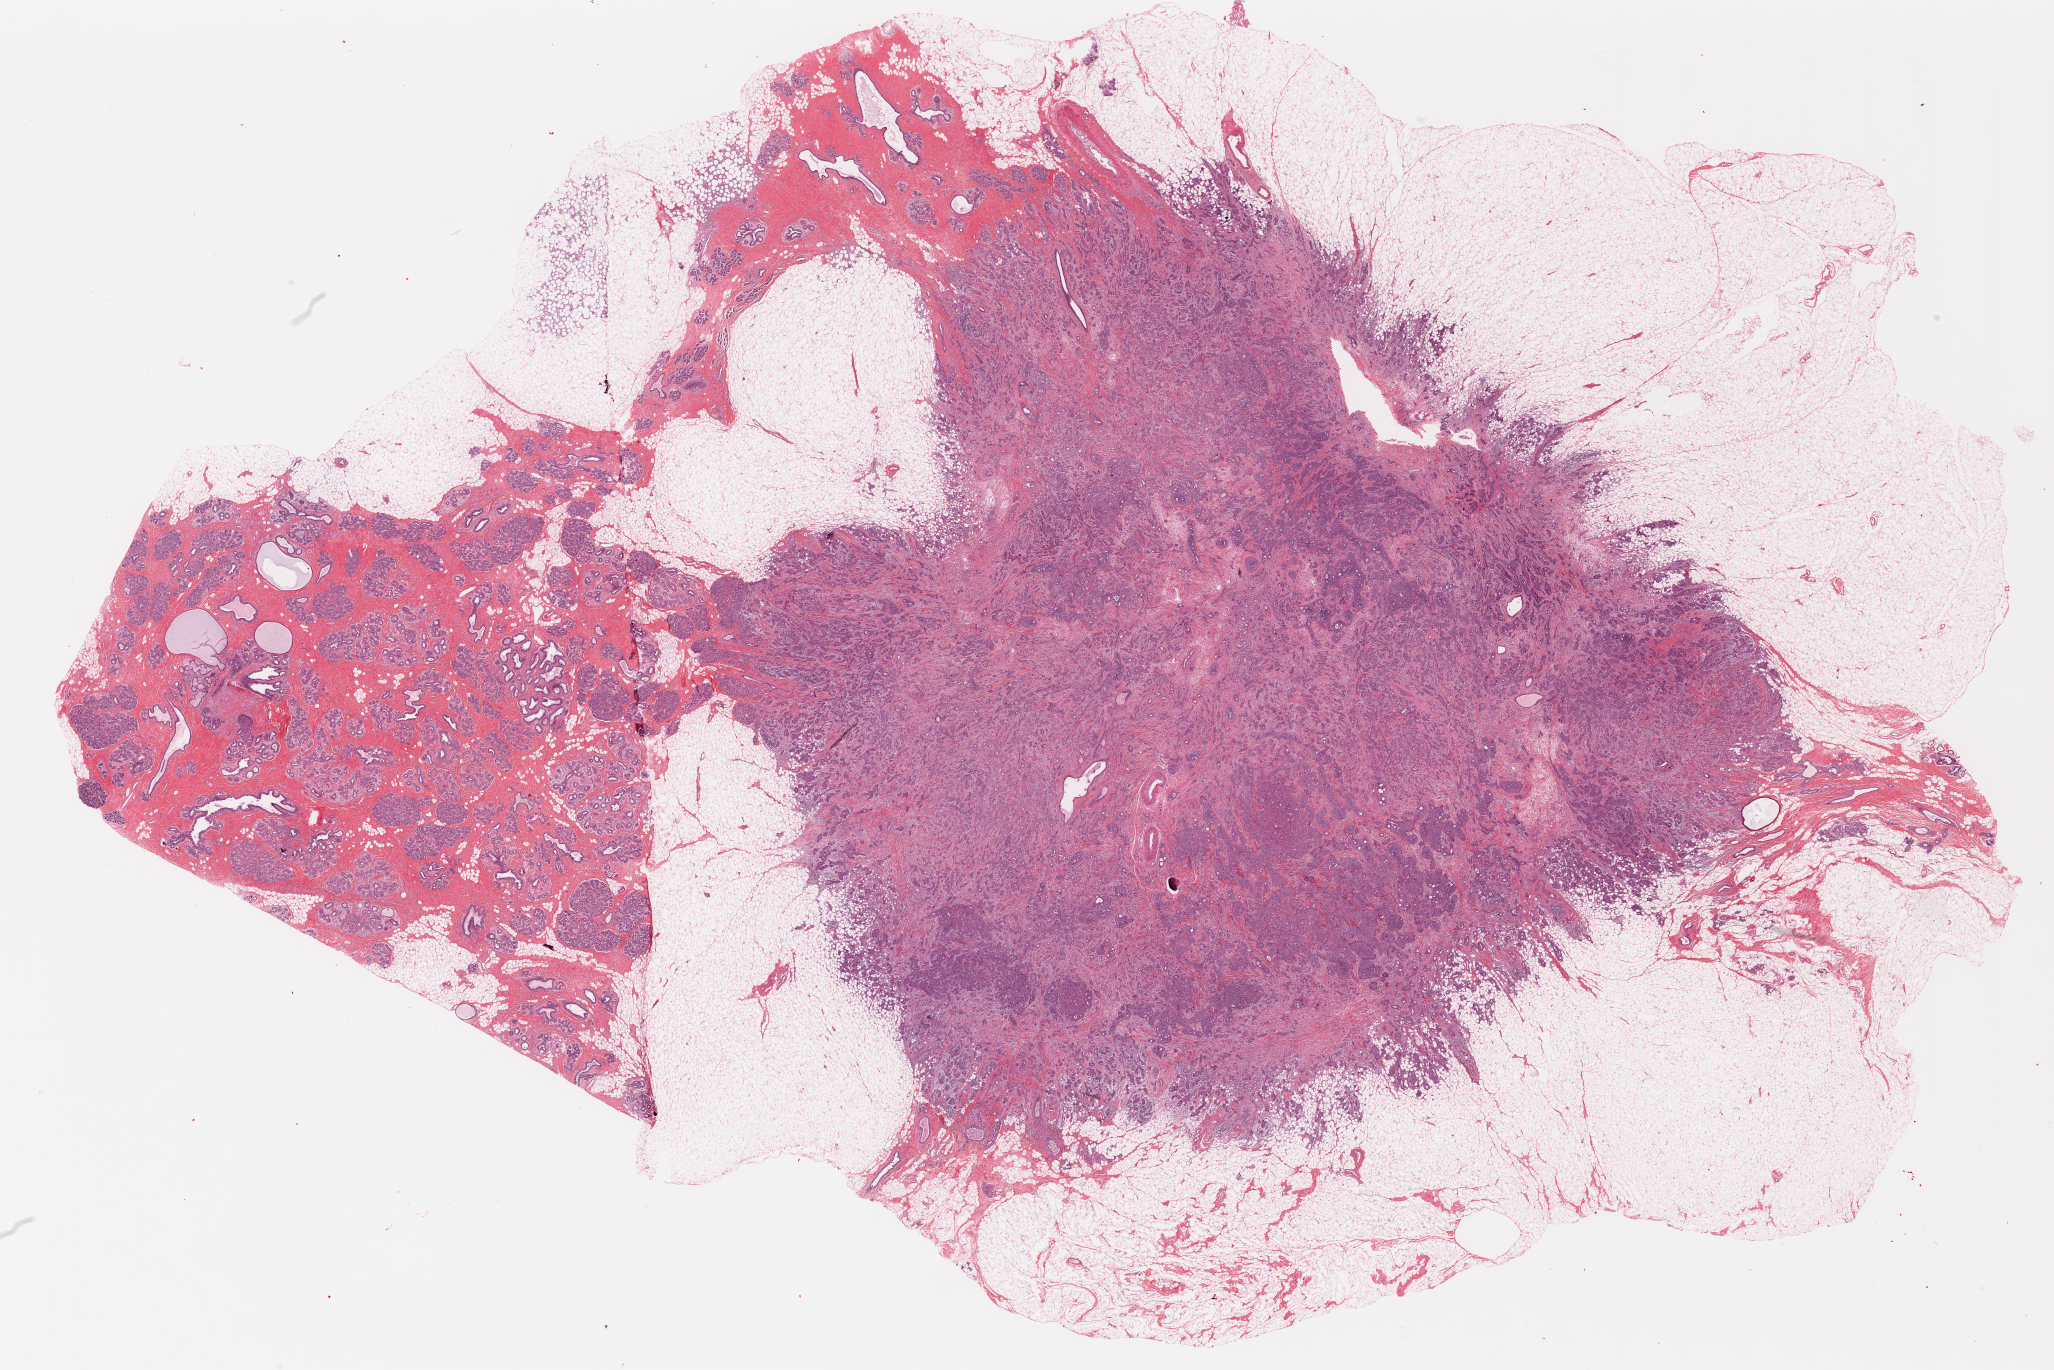
H&E-stained whole-slide image, low-resolution overview of the scanned area, about 32.8 x 21.9 mm (acquisition: 20x scan); formalin-fixed paraffin-embedded (FFPE) diagnostic section; sample: primary tumour, breast. Female, age 47 years at initial diagnosis.
- laterality: right
- pathologic diagnosis: Infiltrating duct carcinoma, NOS
- TNM: T2 N0 (i+) M0
- AJCC pathologic stage: IIA
- lymph nodes positive (case pathology): 0 of 27 examined